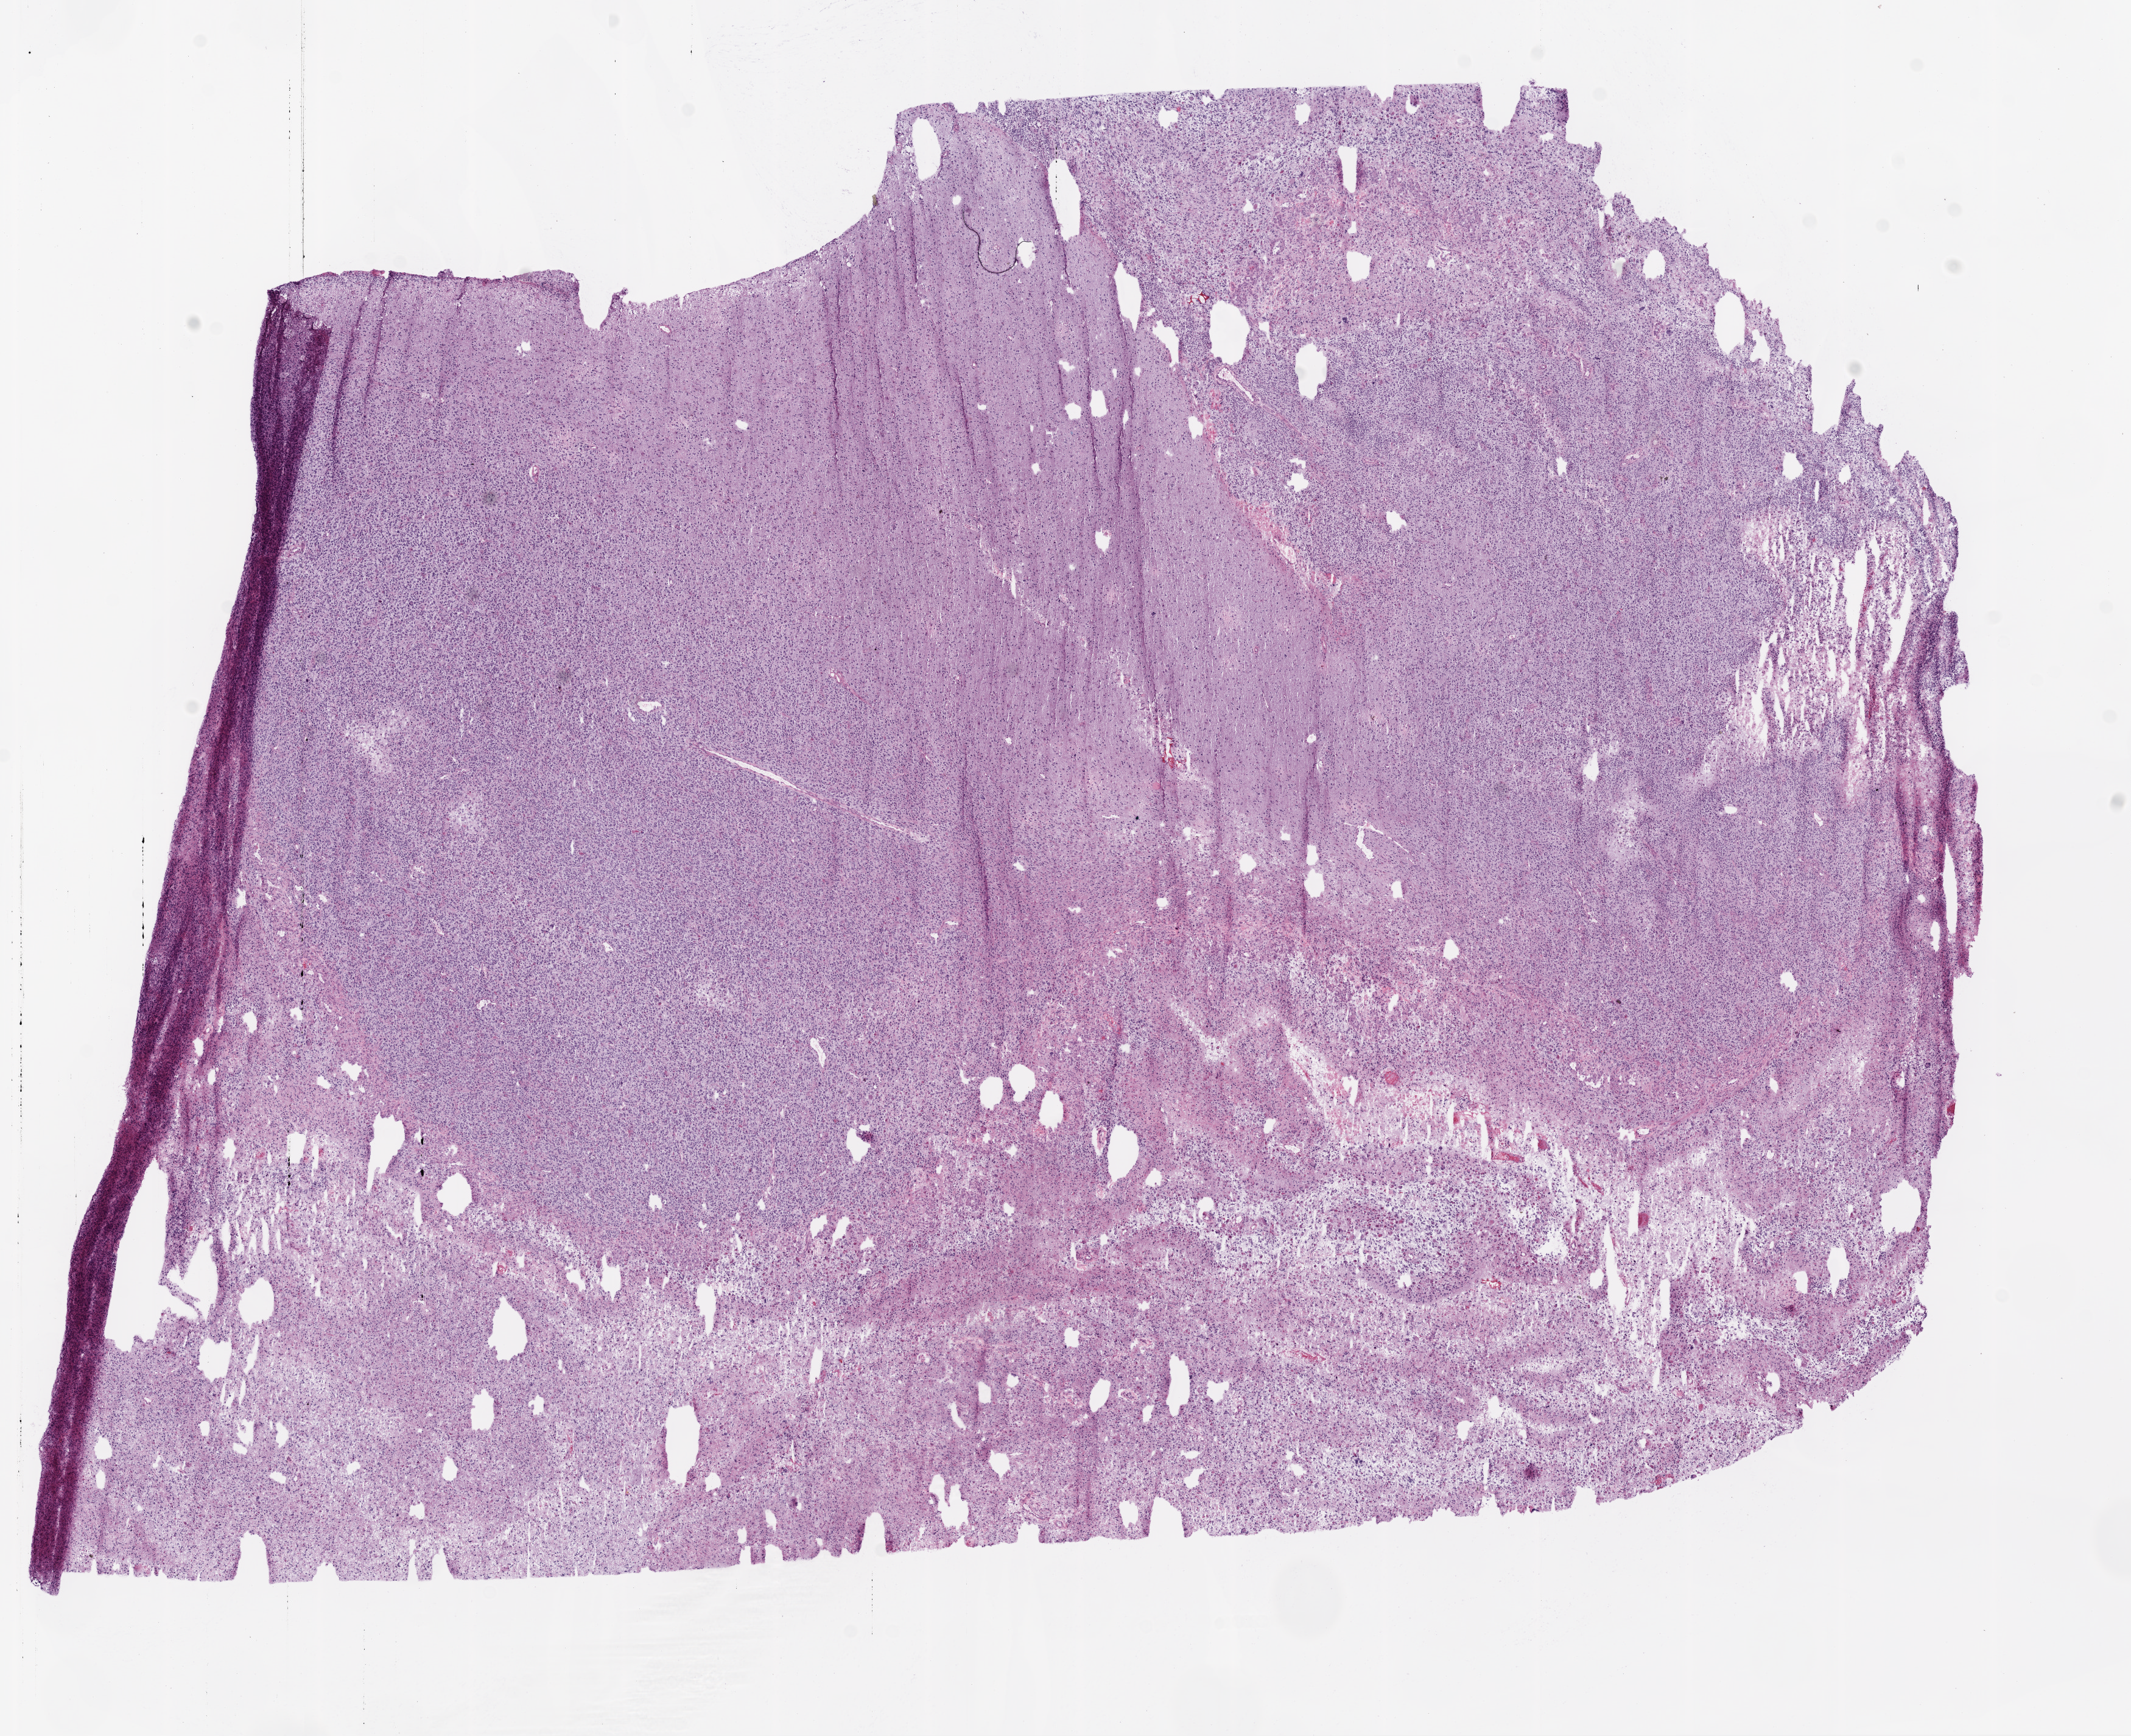
H&E-stained whole-slide image, shown as a low-resolution overview of the whole scanned area (about 14.0 x 11.4 mm), frozen section from the bottom of the tissue portion, primary tumour sample from the brain. Male, age 83 years at initial diagnosis. Pathologist review of this section (percent, as recorded): tumour cells 95%, tumour nuclei 85%, normal cells 0%, stromal cells 0%, necrosis 5%.
• histologic diagnosis: Glioblastoma